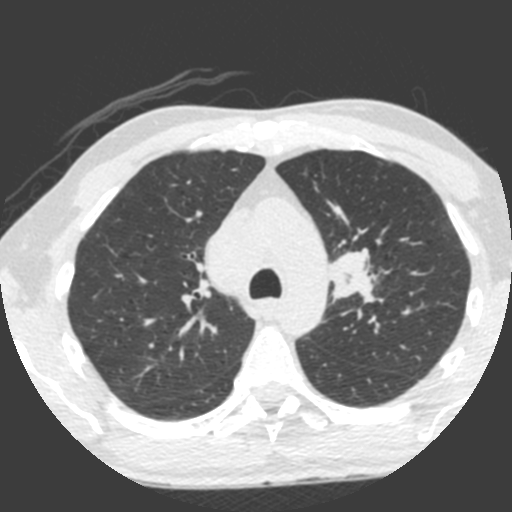
Chest CT (low-dose screening protocol), one axial image; third annual screen; lung window (W 1500 / L -600 HU); 2 mm slice thickness; 120 kVp; 512 × 512 image matrix. Male participant, aged 55 years at enrolment. Current smoker at enrolment.
- Expert-annotated lung lesion, box from (x=308, y=234) to (x=388, y=322) px.
- The exam's reader record, not a measurement of the box and not confirmed to be the same lesion: non-calcified nodule or mass ≥4 mm, left upper lobe, 49 × 29 mm, spiculated (stellate) margins, soft tissue attenuation, pre-existing on the prior screen: yes; interval growth: yes.
- Official screen result: positive, other.
- Participant outcome: lung cancer diagnosed 0 days after this screen — small cell carcinoma, NOS, left upper lobe, undifferentiated (G4), stage IV (AJCC 6th edition), 60 mm at pathology.